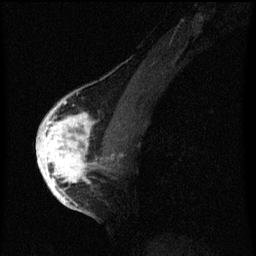
Breast MRI (dynamic contrast-enhanced), one sagittal slice; position 34 of 60 along the scan axis; dynamic contrast-enhanced series, image 2 of 3 at this slice position (ordered by acquisition); 1.5 T; TE 4.2 ms, TR 8 ms; 2 mm slice thickness; 256 × 256 image matrix, field of view 180 × 180 mm. Female patient, age 56 years.
Outlined on this slice (semi-automatic segmentation, software-assisted and operator-edited):
- analysis volume of interest (the breast-tissue region the enhancement analysis was run in; not a lesion): bounding box <42,110,97,193> (left, top, right, bottom; pixels)
- tumour enhancement mask (voxels above the 70 % enhancement threshold inside the analysis volume of interest): <42,110,95,193>